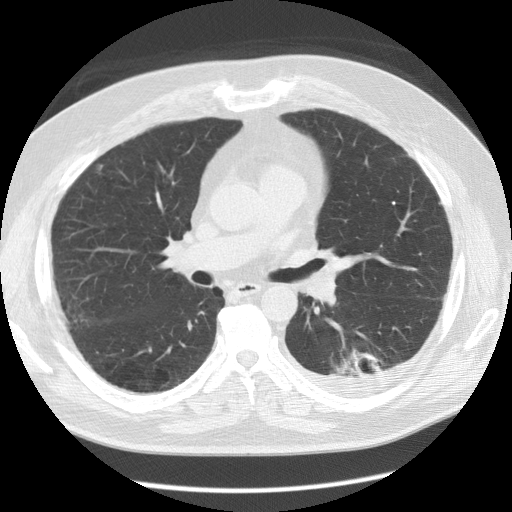
Low-dose screening chest CT, one axial slice; 120 kVp; lung window (W 1500 / L -600 HU); 2.5 mm slice thickness; 512 × 512 image matrix, field of view 370 × 370 mm.
Annotated regions visible in this slice (outlined manually by an expert reader):
- lesion 1 (tumor, lower lobe of left lung): bounding box [x1, y1, x2, y2] px = [339, 349, 382, 376]